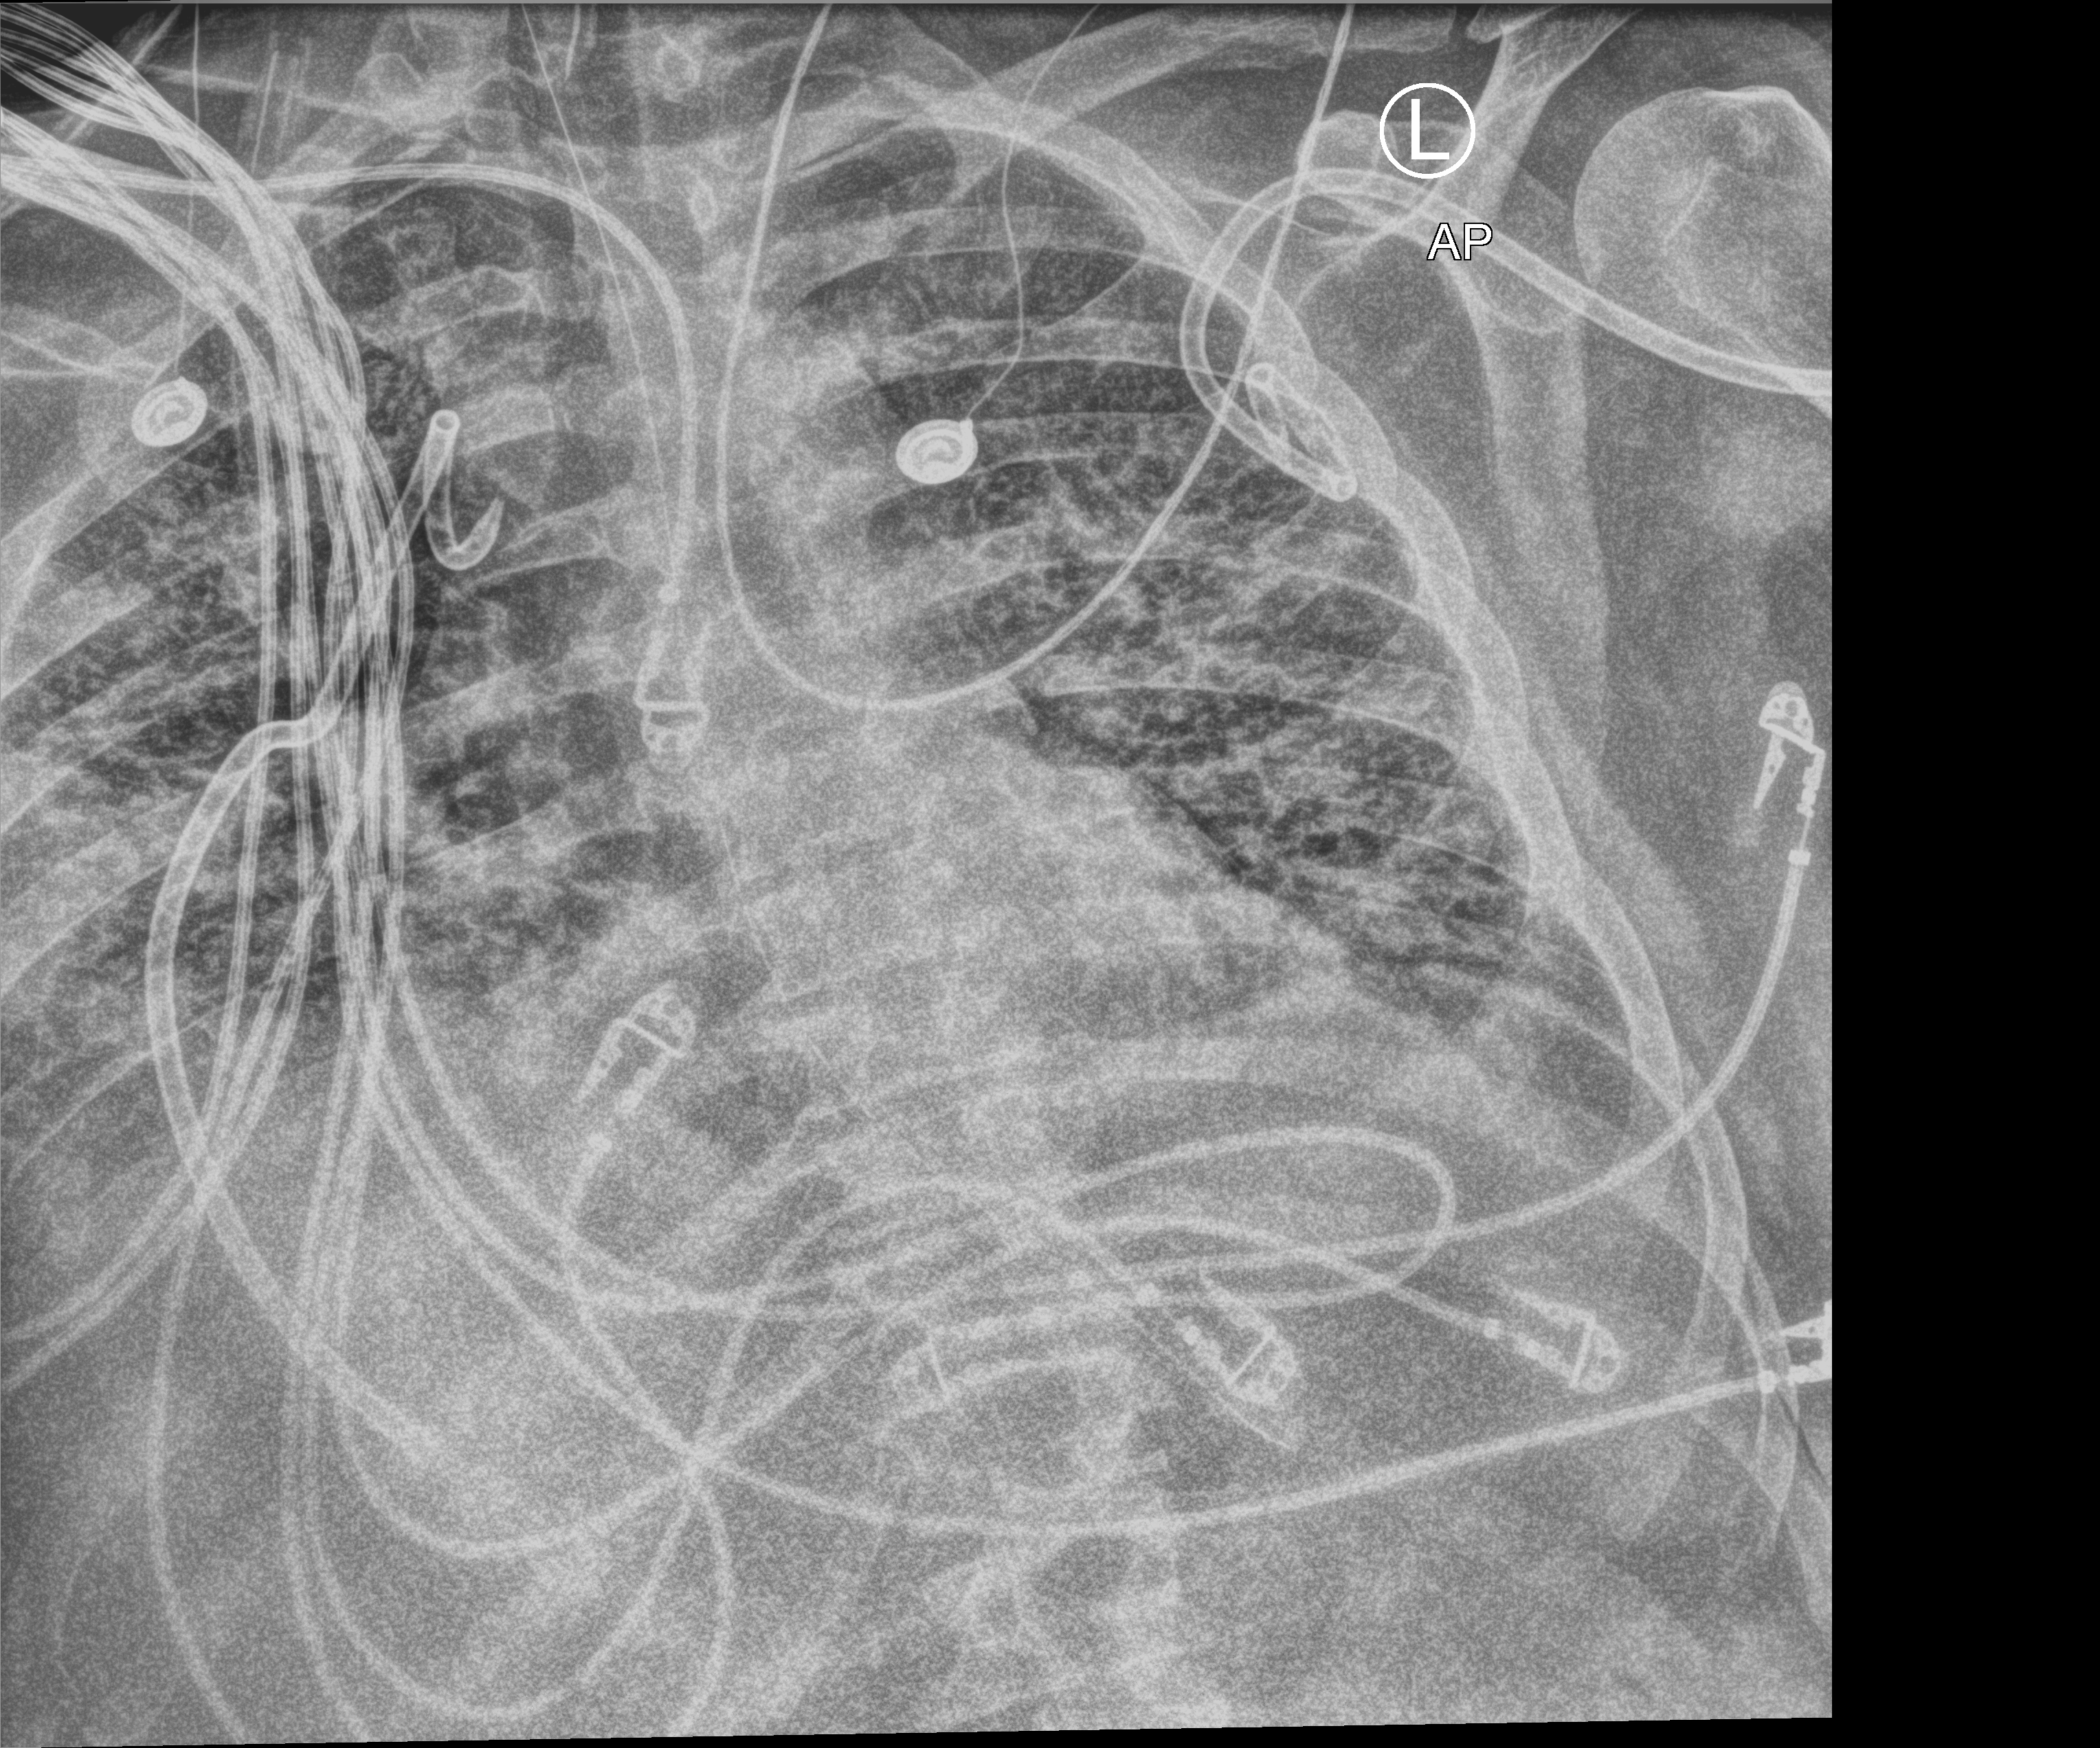
Portable chest radiograph, anteroposterior (AP) projection. Adult patient hospitalised with COVID-19, age 18–59 years.
Admission-level facts for this patient (not findings on this image; timing relative to this image not recorded): admitted to intensive care during this hospital stay: yes.